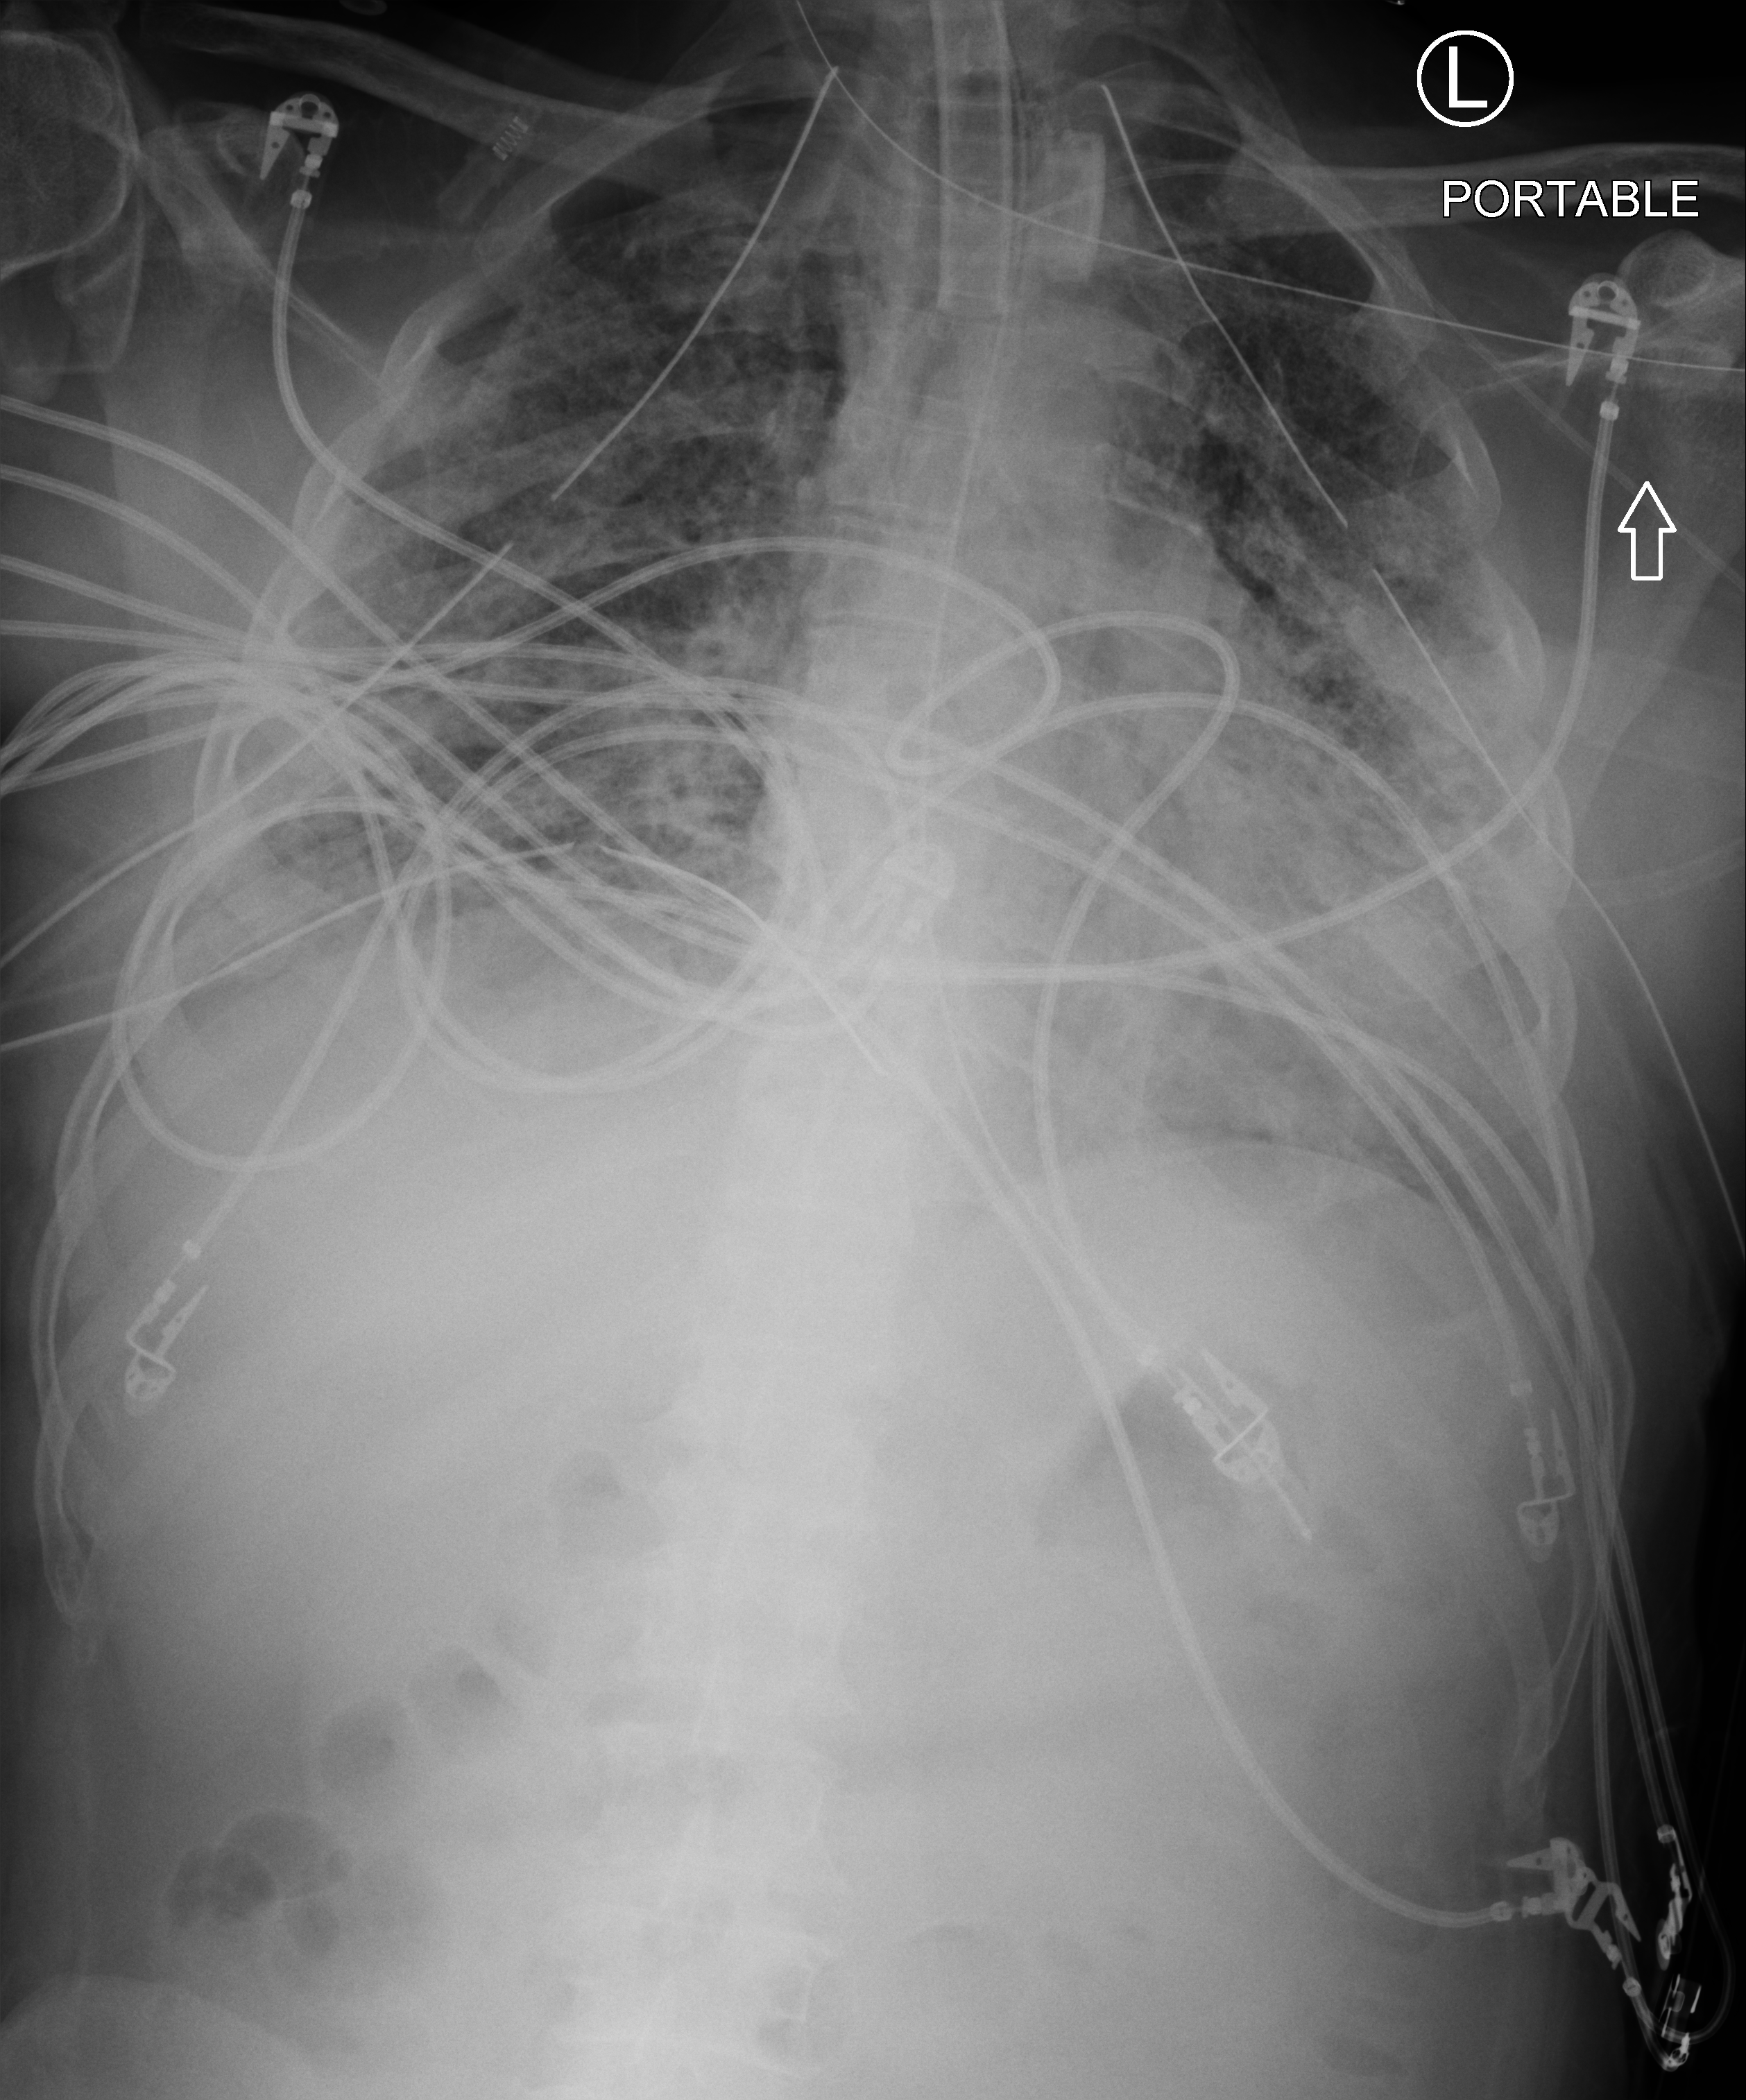
Bedside chest radiograph (computed radiography); anteroposterior (AP) projection. Patient hospitalised with COVID-19; male, aged 18–59 years.
Hospital-stay facts (about this admission, not read from this image; timing relative to this image not recorded):
- mechanically ventilated during this hospital stay: yes
- length of hospital stay: 83 days
- admitted to intensive care during this hospital stay: yes